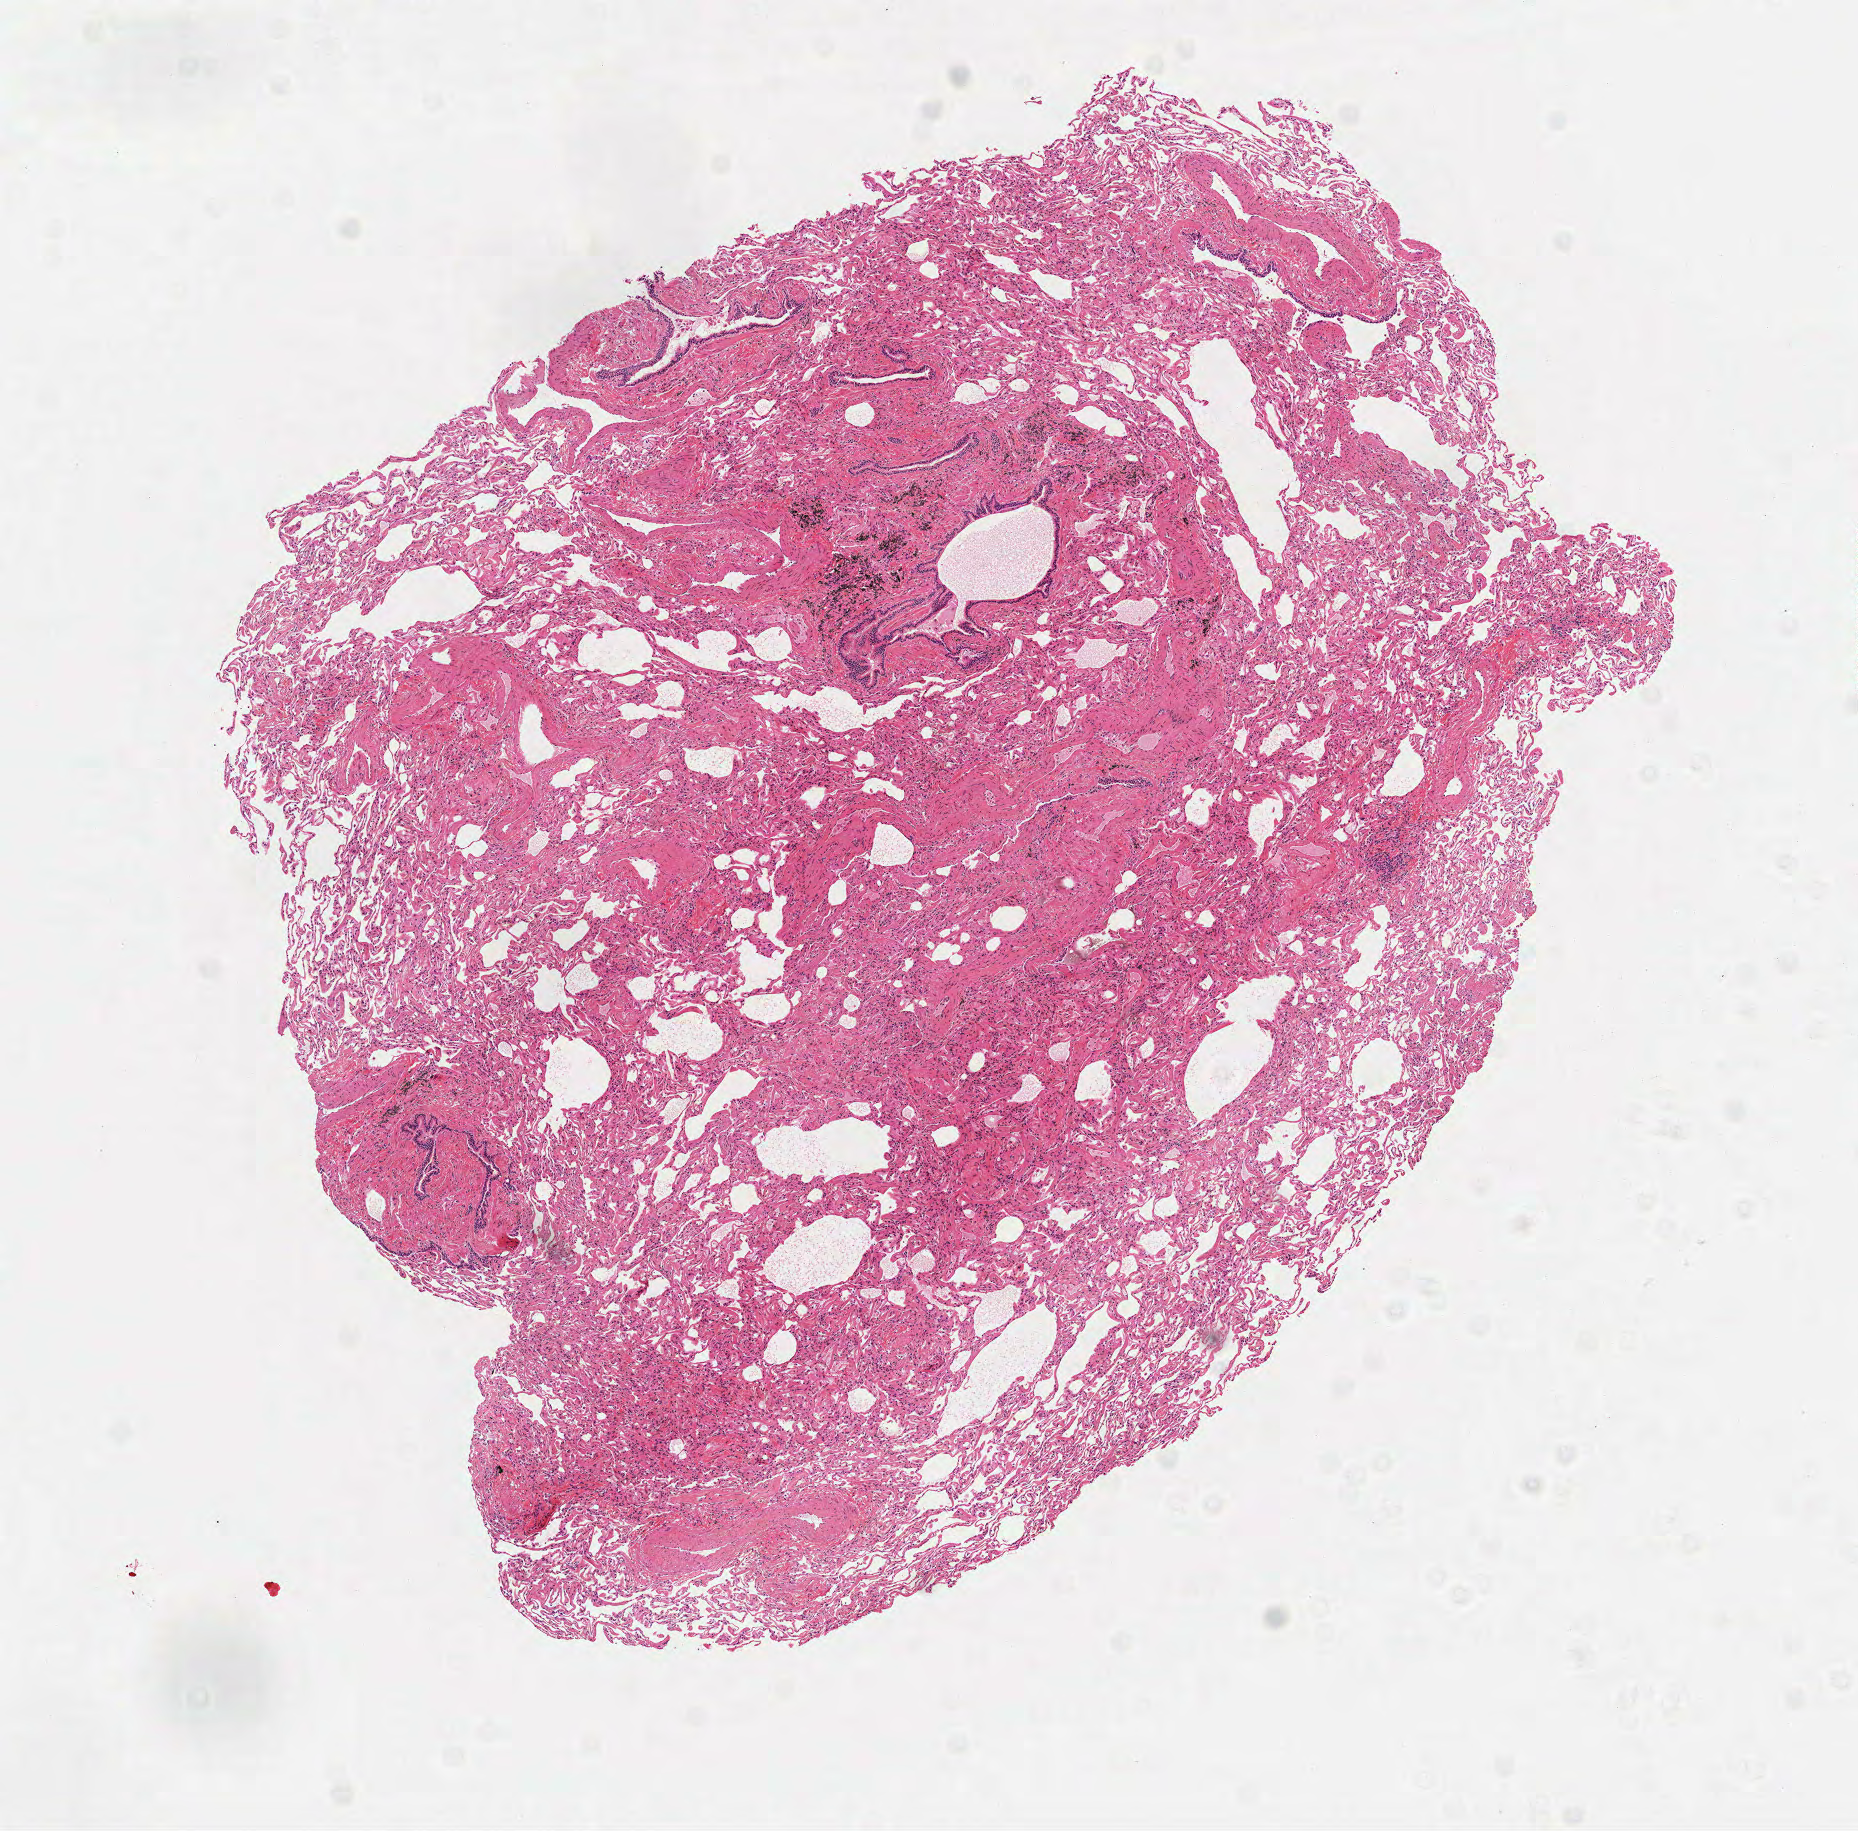
Digitized H&E tissue section (whole slide) — a low-resolution overview of the entire scanned area, about 7.5 x 7.4 mm; frozen section from the top of the tissue portion; sample: solid tissue normal (non-tumour tissue), lung. Female patient; age at initial diagnosis 66 years.
This section: solid tissue normal (non-tumour) sample from the same patient. Patient diagnosis: Bronchio-alveolar carcinoma, mucinous.